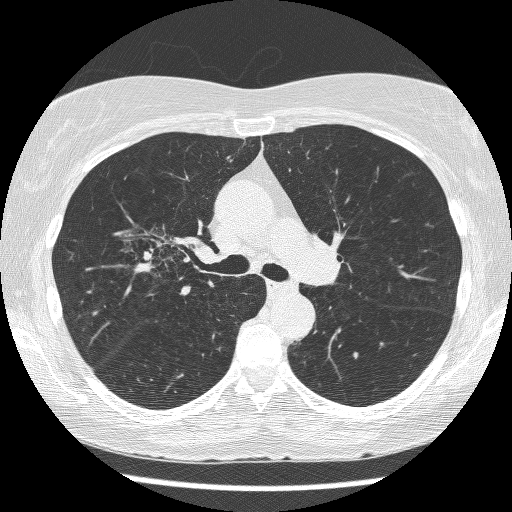
Chest CT (low-dose screening protocol), one axial image. Baseline annual screen. Lung window (W 1500 / L -600 HU). Lung (sharp) reconstruction kernel (BONE). Slice 177 of 271 in the series. 512 × 512 image matrix, field of view 316 × 316 mm. Female participant, aged 64 years at enrolment. Former smoker at enrolment.
Expert reader's lesion annotation, bounding box (x1, y1, x2, y2) in pixels: (125, 222, 204, 293). The screening reader recorded 3 non-calcified nodules or masses ≥4 mm on this exam; which of them this box marks is not recorded. Official screen result: positive, change unspecified: nodule(s) >= 4 mm or enlarging nodule(s), mass(es), or other non-specific abnormalities suspicious for lung cancer. Lung cancer was diagnosed 735 days after this screen: adenocarcinoma, NOS, right upper lobe, right middle lobe, right hilum, stage IV (AJCC 6th edition), 85 mm at pathology.